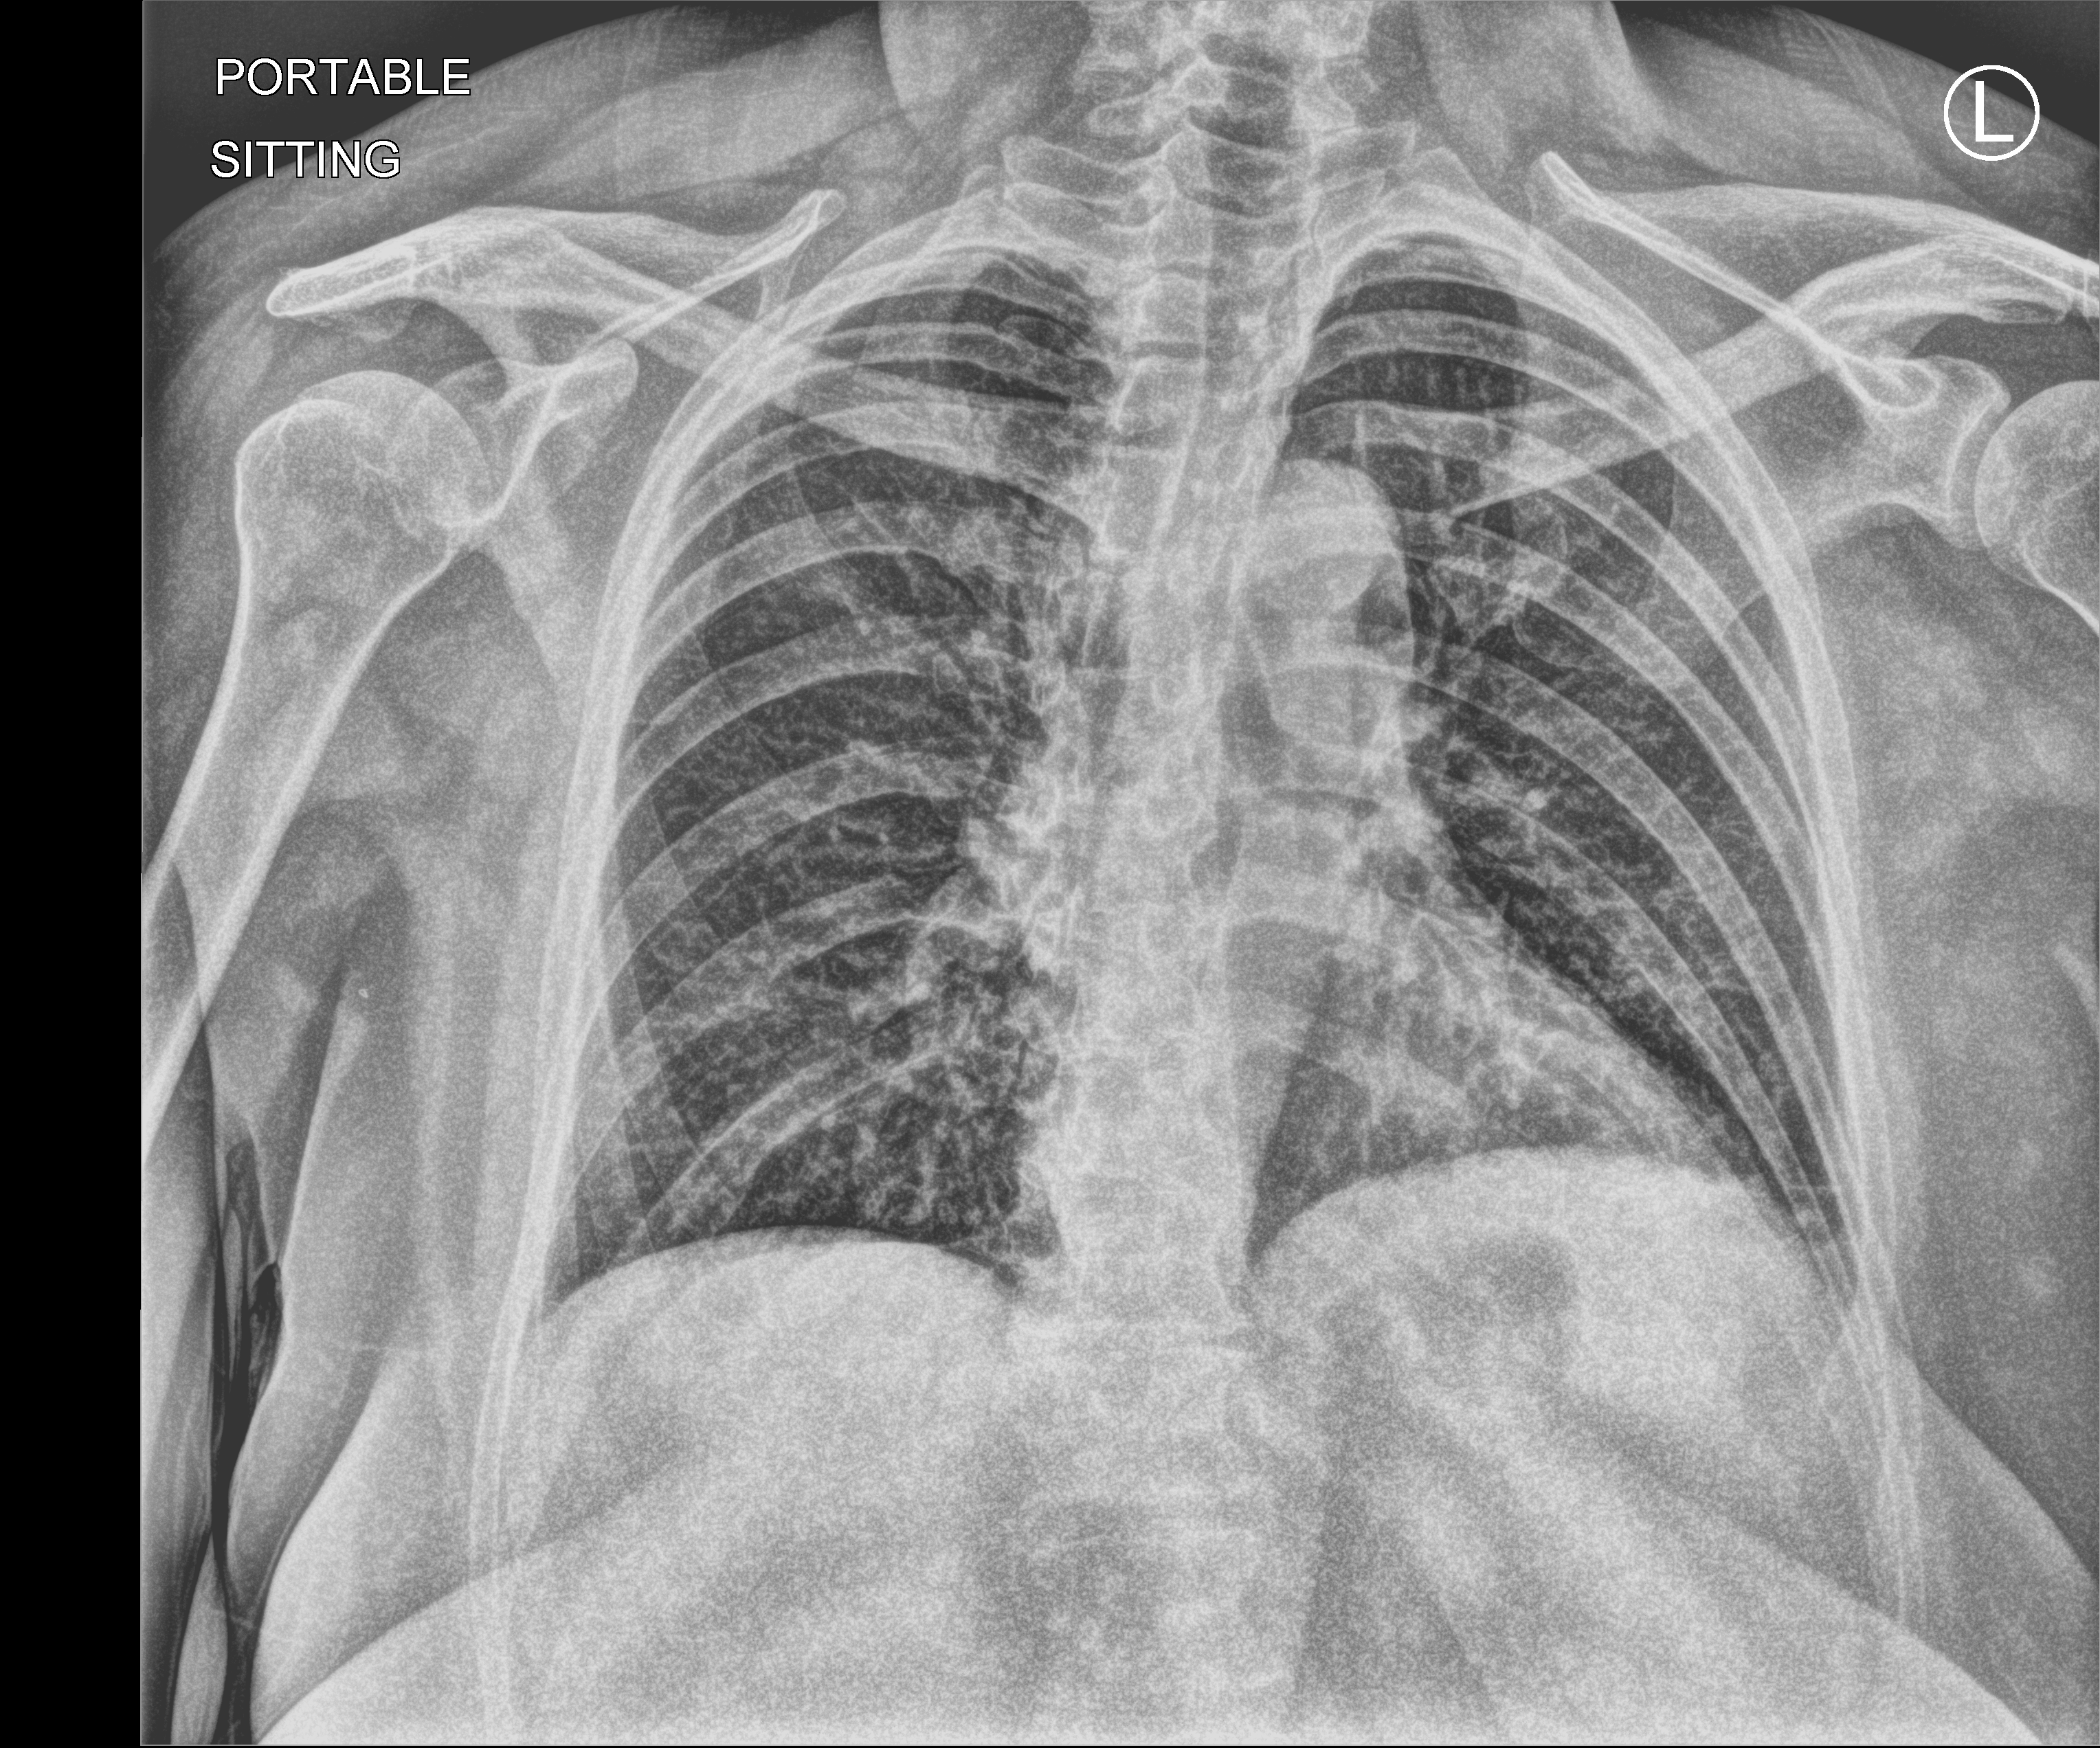
Portable chest radiograph, anteroposterior (AP) projection. Patient hospitalised with COVID-19; female, aged 18–59 years.
Hospital-stay facts (about this admission, not read from this image; timing relative to this image not recorded):
- hypertension (admission record): no
- length of hospital stay: 8 days
- mechanically ventilated during this hospital stay: no